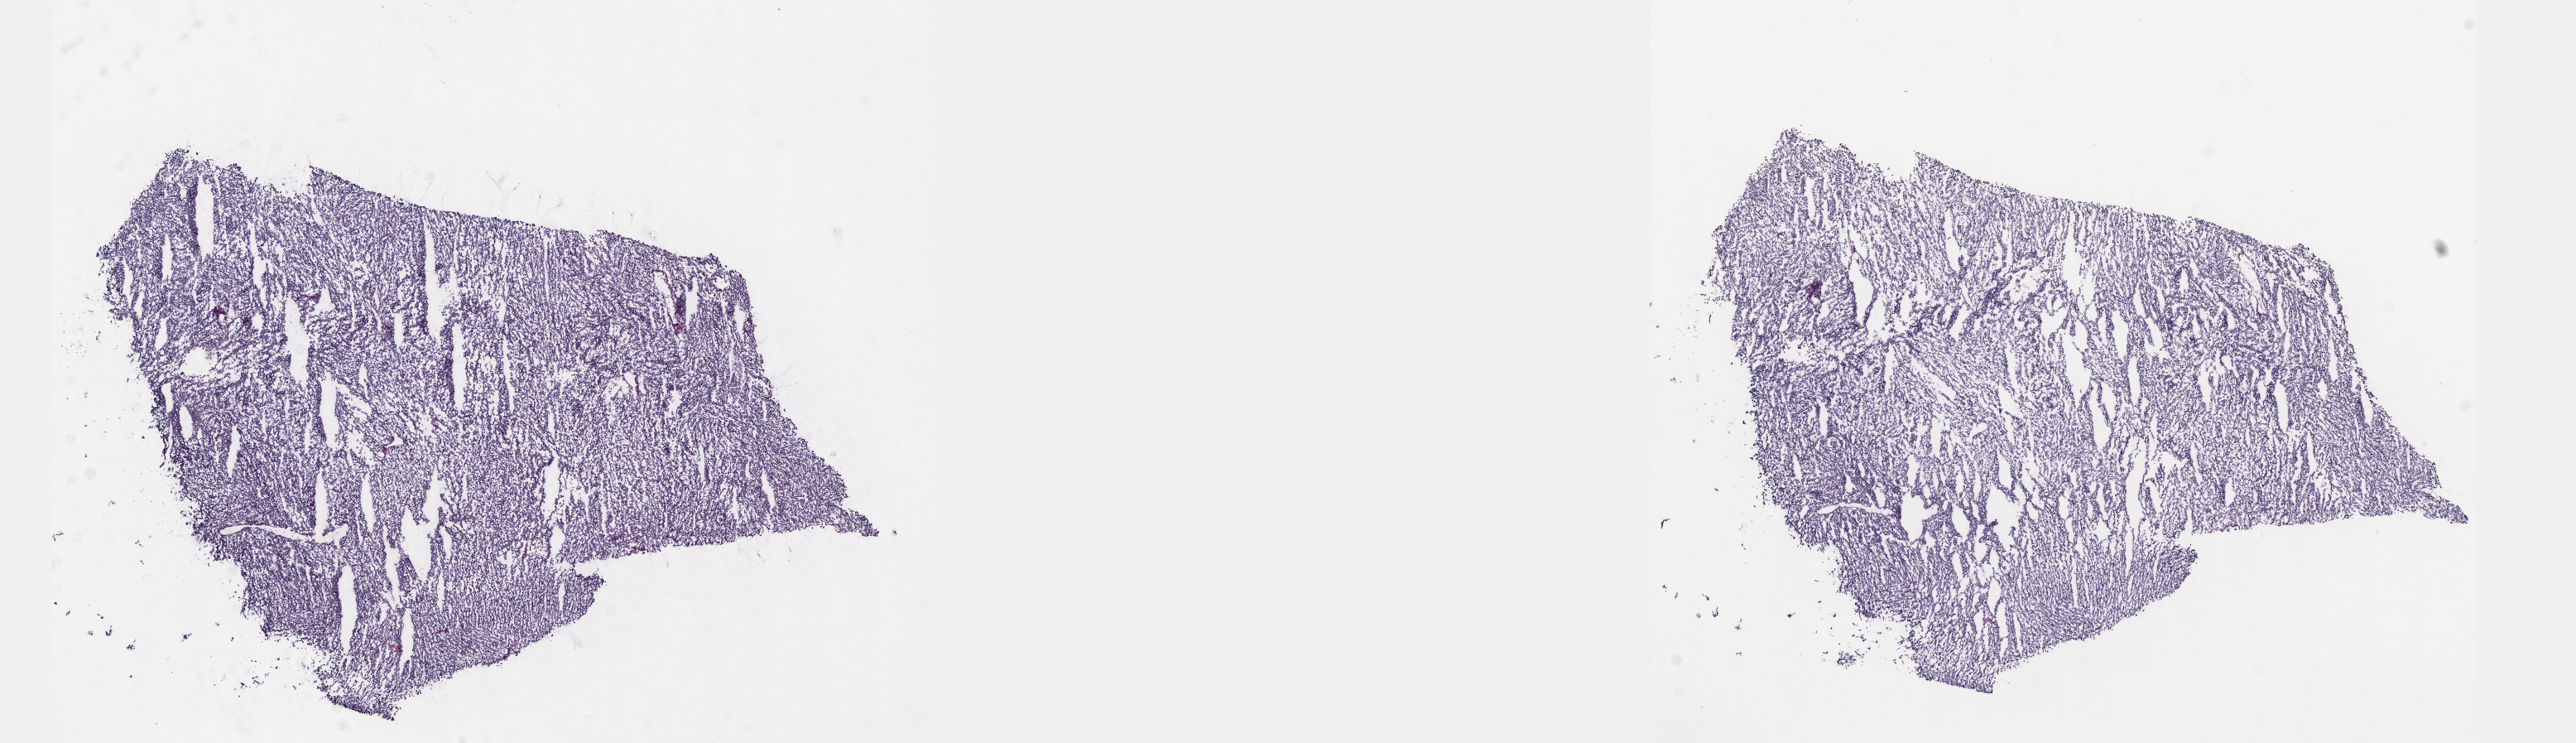
Digitized H&E-stained tissue section (whole slide), shown as a low-resolution overview of the whole scanned area (about 25.1 x 7.2 mm, acquisition: 40x scan), frozen section, testis, primary tumour sample. Male, age 33 years at initial diagnosis. Pathologist review of this section (percent, as recorded): tumour cells 100%, tumour nuclei 80%, normal cells 0%, stromal cells 0%, necrosis 0%. Inflammatory infiltration, as recorded: lymphocyte infiltration 0%, monocyte infiltration 0%, neutrophil infiltration 0%.
TNM: T2 NX M0. AJCC pathologic stage: I (6th edition). Histologic diagnosis: Seminoma, NOS. Laterality: right.